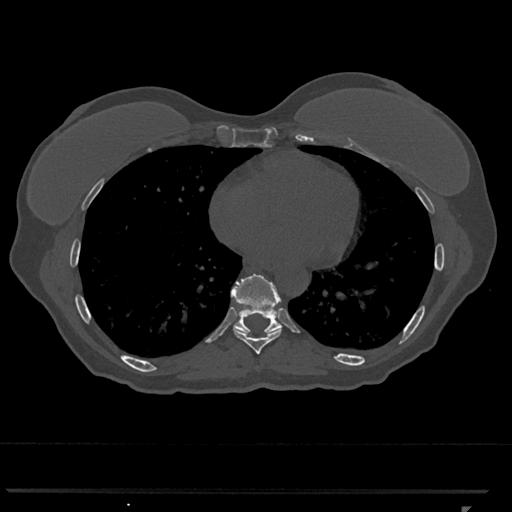
CT including the spine, one axial slice. Slice 647 of 793 in the series (ordered by position). Reconstruction kernel Br40s/3. Bone window (W 1800 / L 400 HU). 0.5 mm slice thickness. 512 × 512 image matrix, field of view 380 × 380 mm. Patient: female, 62 years. Case-level facts recorded for this patient, not image findings: primary cancer: renal.
Structures marked on this image (semi-automatically segmented with operator editing):
- T8 vertebra: bounding box <233,328,282,354> (left, top, right, bottom; pixels)
- T9 vertebra: <231,274,282,335>